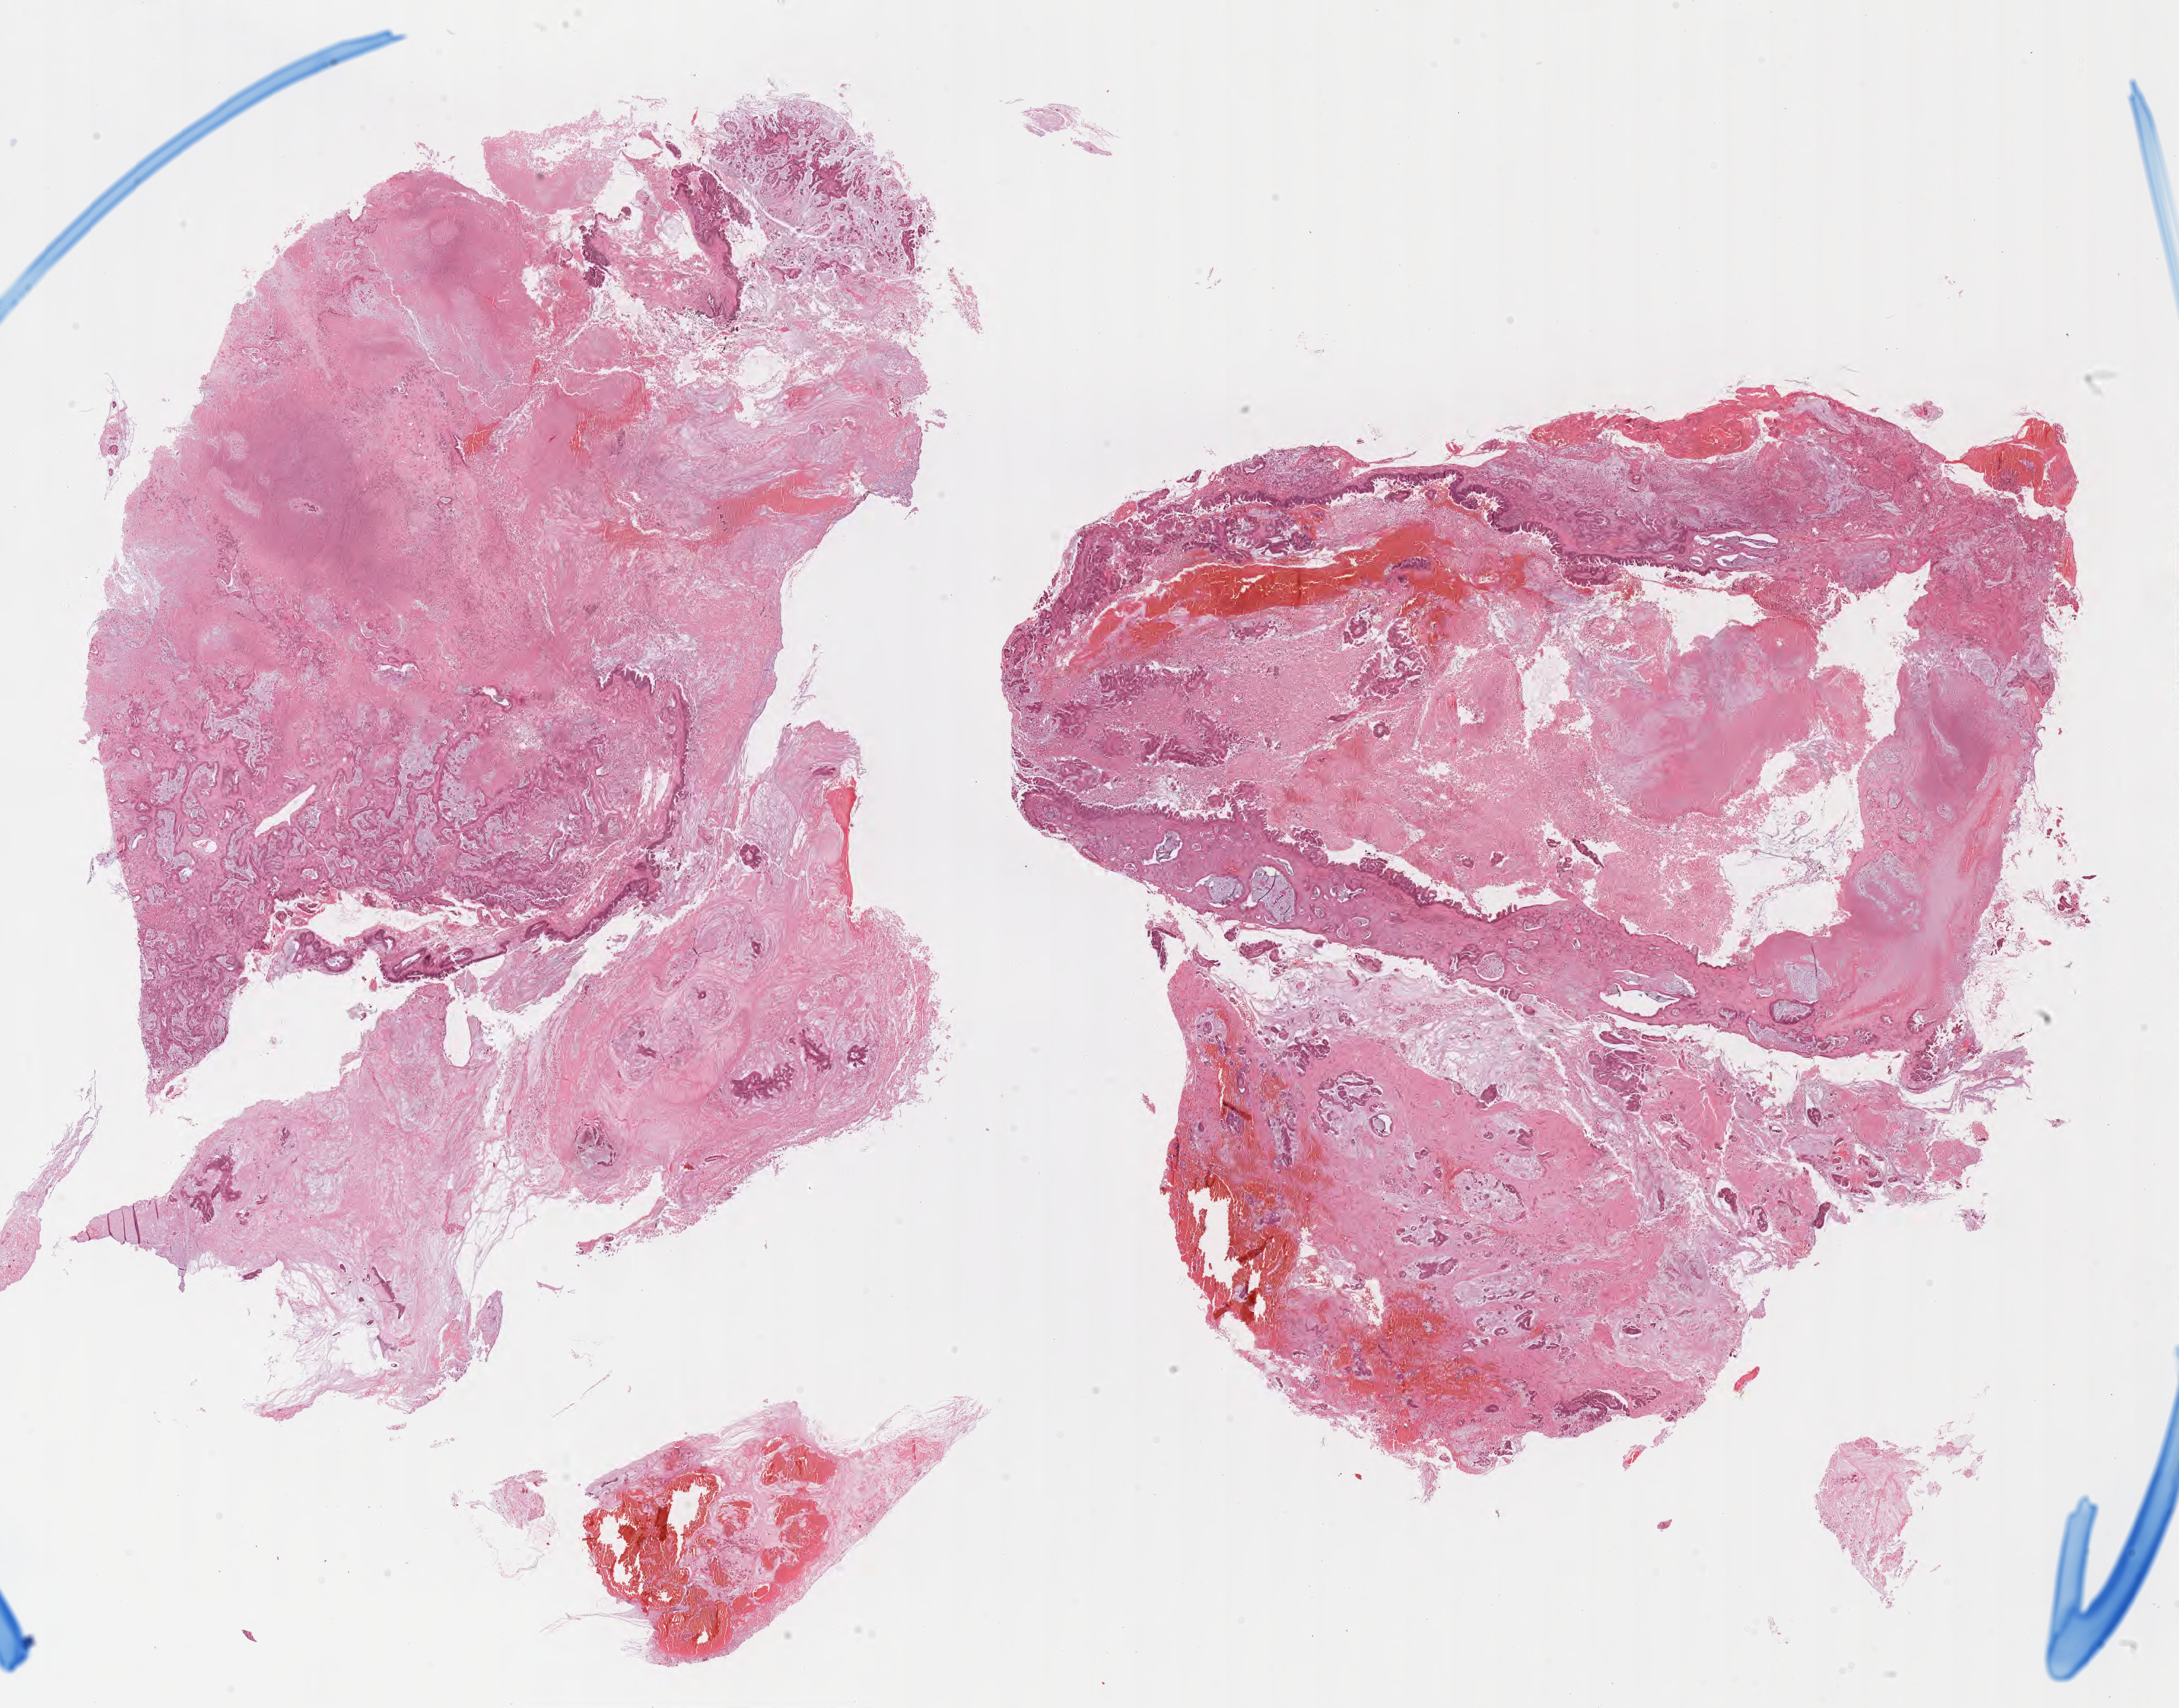
H&E whole-slide image — whole scanned area (about 24.2 x 18.9 mm) shown as a low-resolution overview, FFPE section, specimen: metastatic tumor tissue, resected from brain. Patient: male, age at initial diagnosis 68 years. Slide review estimates, as recorded: tumor cells 50%, tumor nuclei 50%, stromal cells 15%, necrosis 35%, normal cells 0%. Infiltration values recorded for this section: lymphocyte infiltration 3%, monocyte infiltration 2%, neutrophil infiltration 6%.
* patient diagnosis (primary): Small cell carcinoma, NOS